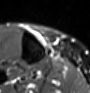
MRI of an extremity soft-tissue mass, one axial slice; position 14 of 60 along the scan axis; STIR; MR volume resampled by the dataset authors to the PET/CT grid (not the native acquisition matrix); 3.27 mm slice thickness; 90 × 93 image matrix, field of view 88 × 91 mm. Female patient. Case-level facts recorded for this patient, not image findings: histological type: undifferentiated – high grade; grade: high; site of the primary tumour: right thigh.
Annotated regions visible in this slice (expert contour drawn on MRI and transferred to this co-registered scan by the dataset authors):
- gross tumour volume (mass): bounding box [x1, y1, x2, y2] px = [37, 33, 48, 45]